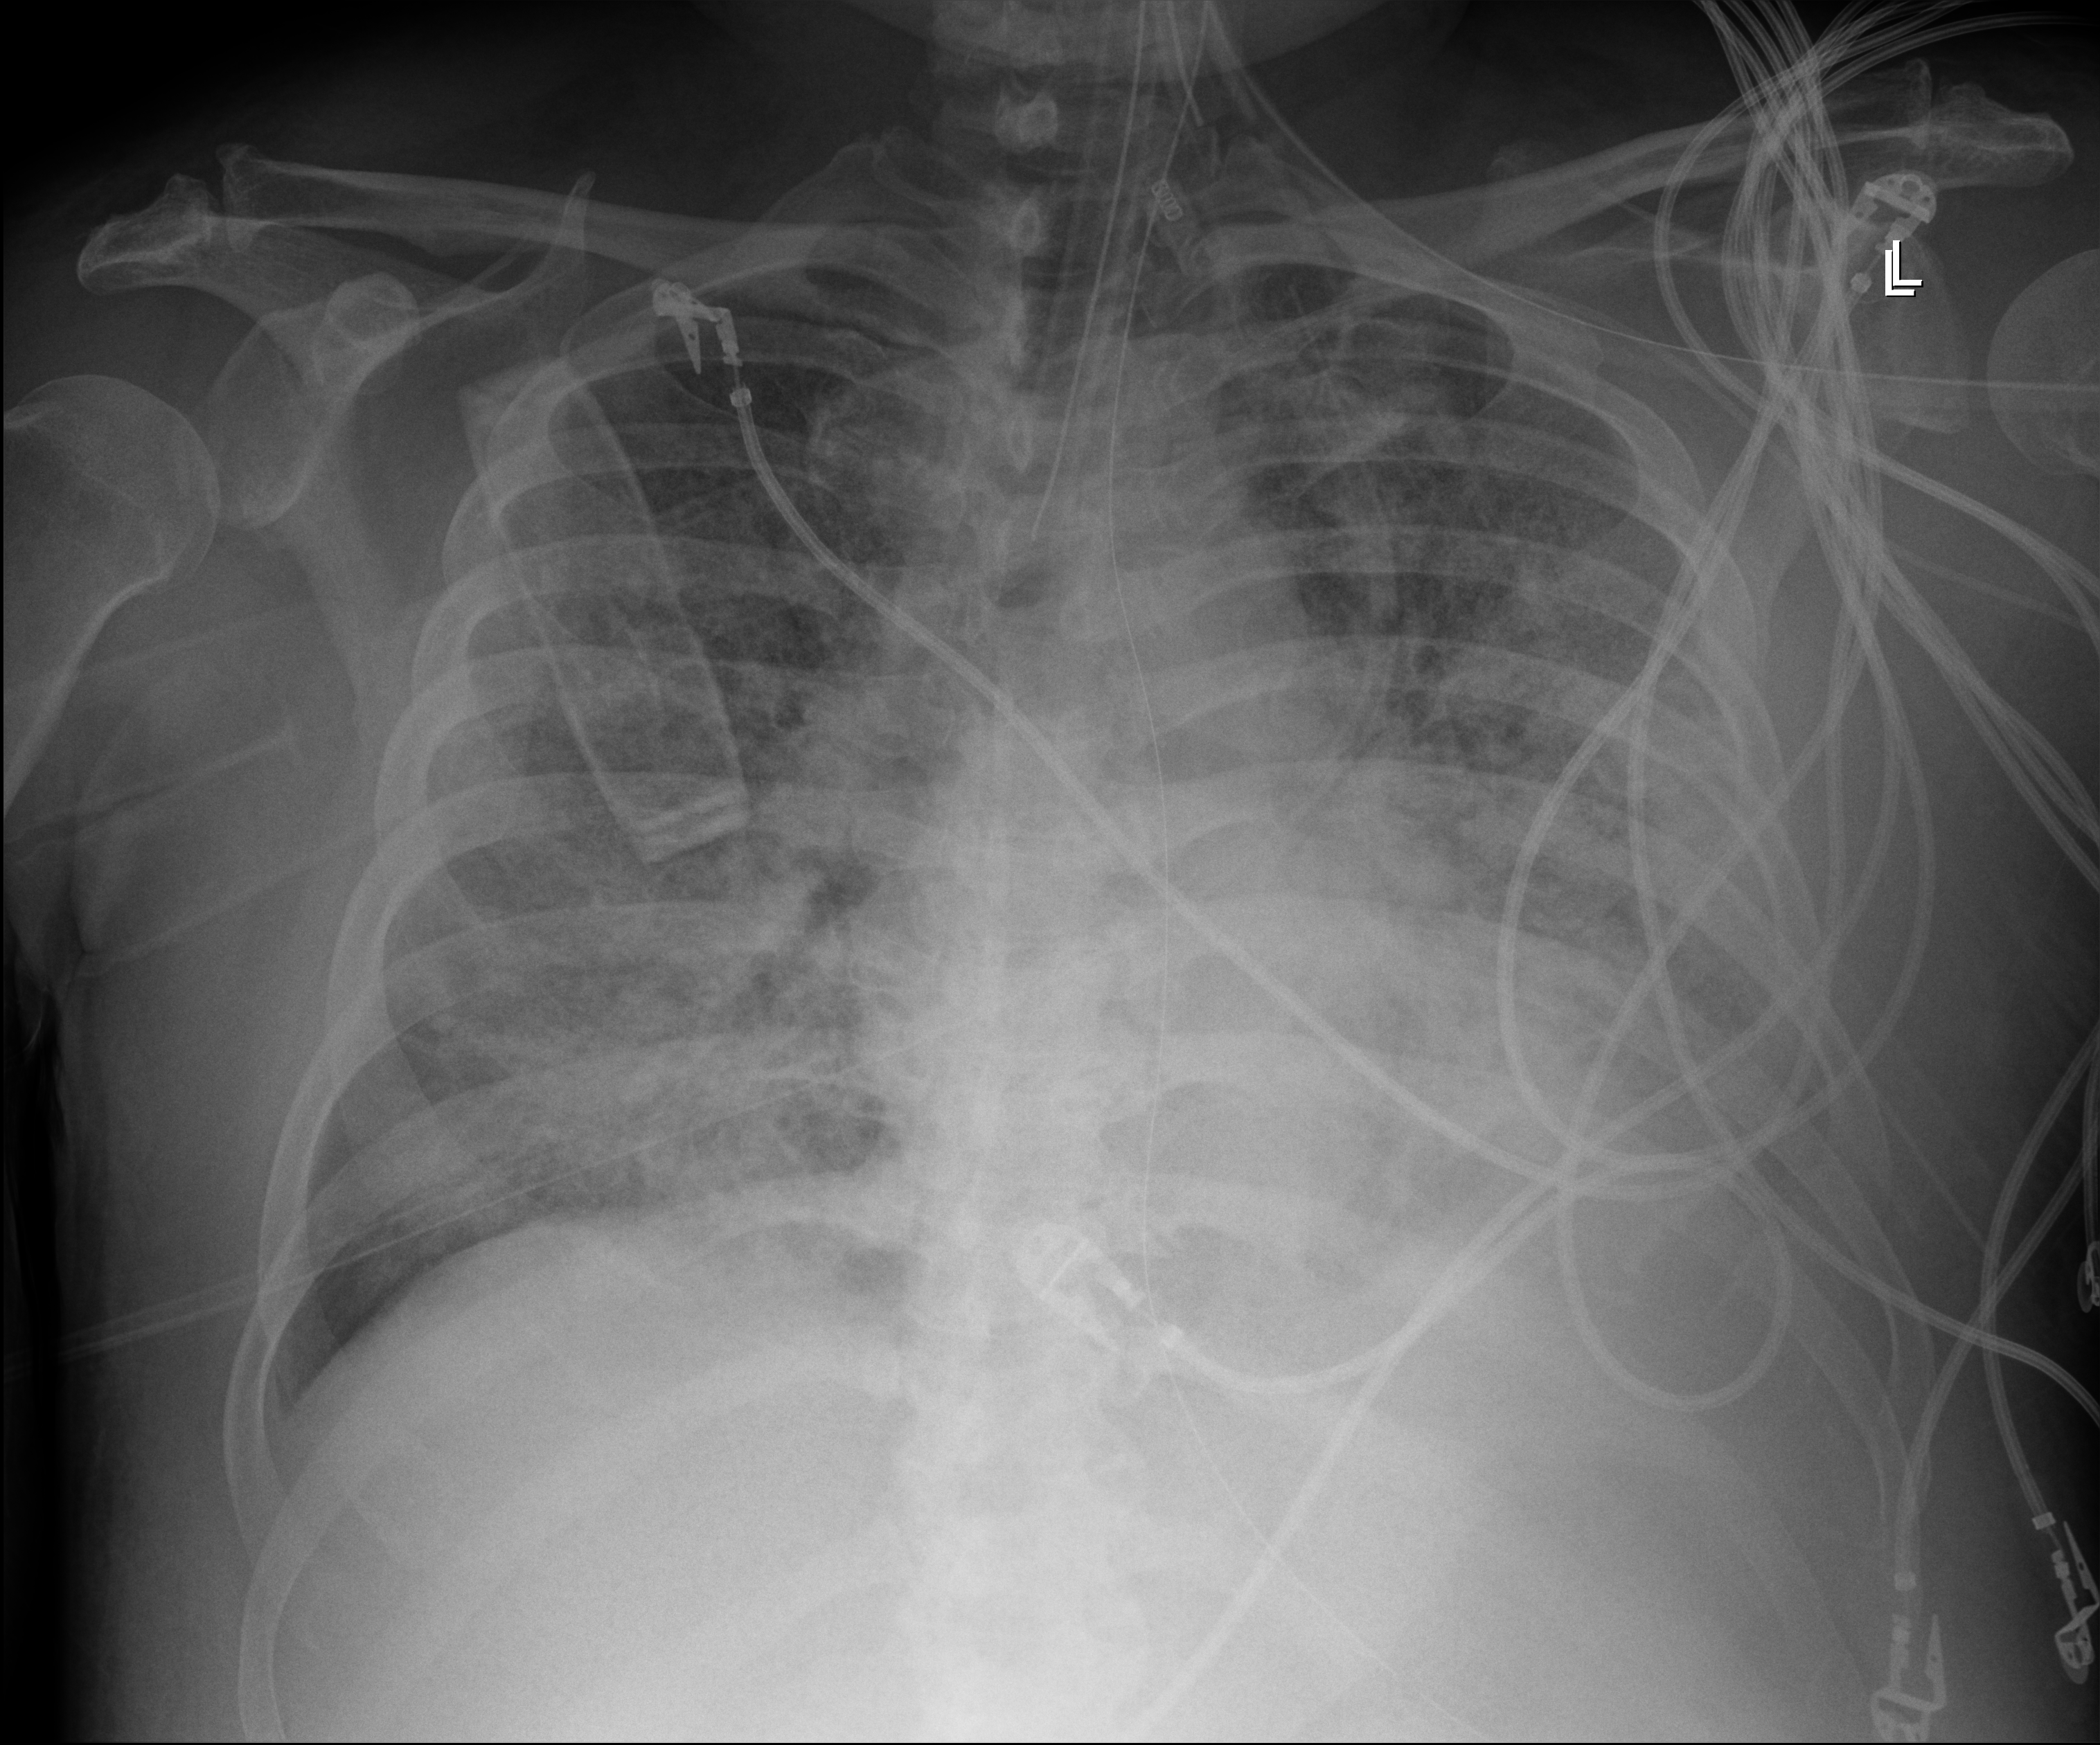
Chest X-ray (portable); anteroposterior (AP) projection. Patient hospitalised with COVID-19; male, aged 60–74 years.
Hospital-stay facts (about this admission, not read from this image; timing relative to this image not recorded): admitted to intensive care during this hospital stay: yes.